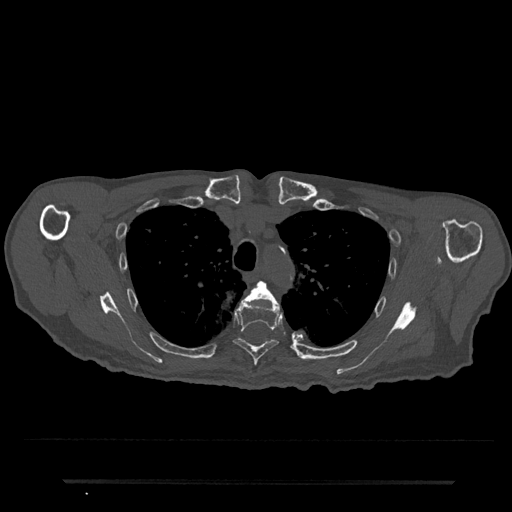
CT including the spine, one axial slice. 120 kVp. Bone window (W 1800 / L 400 HU). 0.5 mm slice thickness. 512 × 512 image matrix, field of view 427 × 427 mm. Patient: male, 74 years. Case-level facts recorded for this patient, not image findings: primary cancer: prostate.
Annotated regions visible in this slice (semi-automatically segmented with operator editing):
- T4 vertebra: bounding box [x1, y1, x2, y2] px = [246, 281, 277, 303]
- T5 vertebra: [233, 298, 282, 366]
- T6 vertebra: [264, 339, 267, 343]